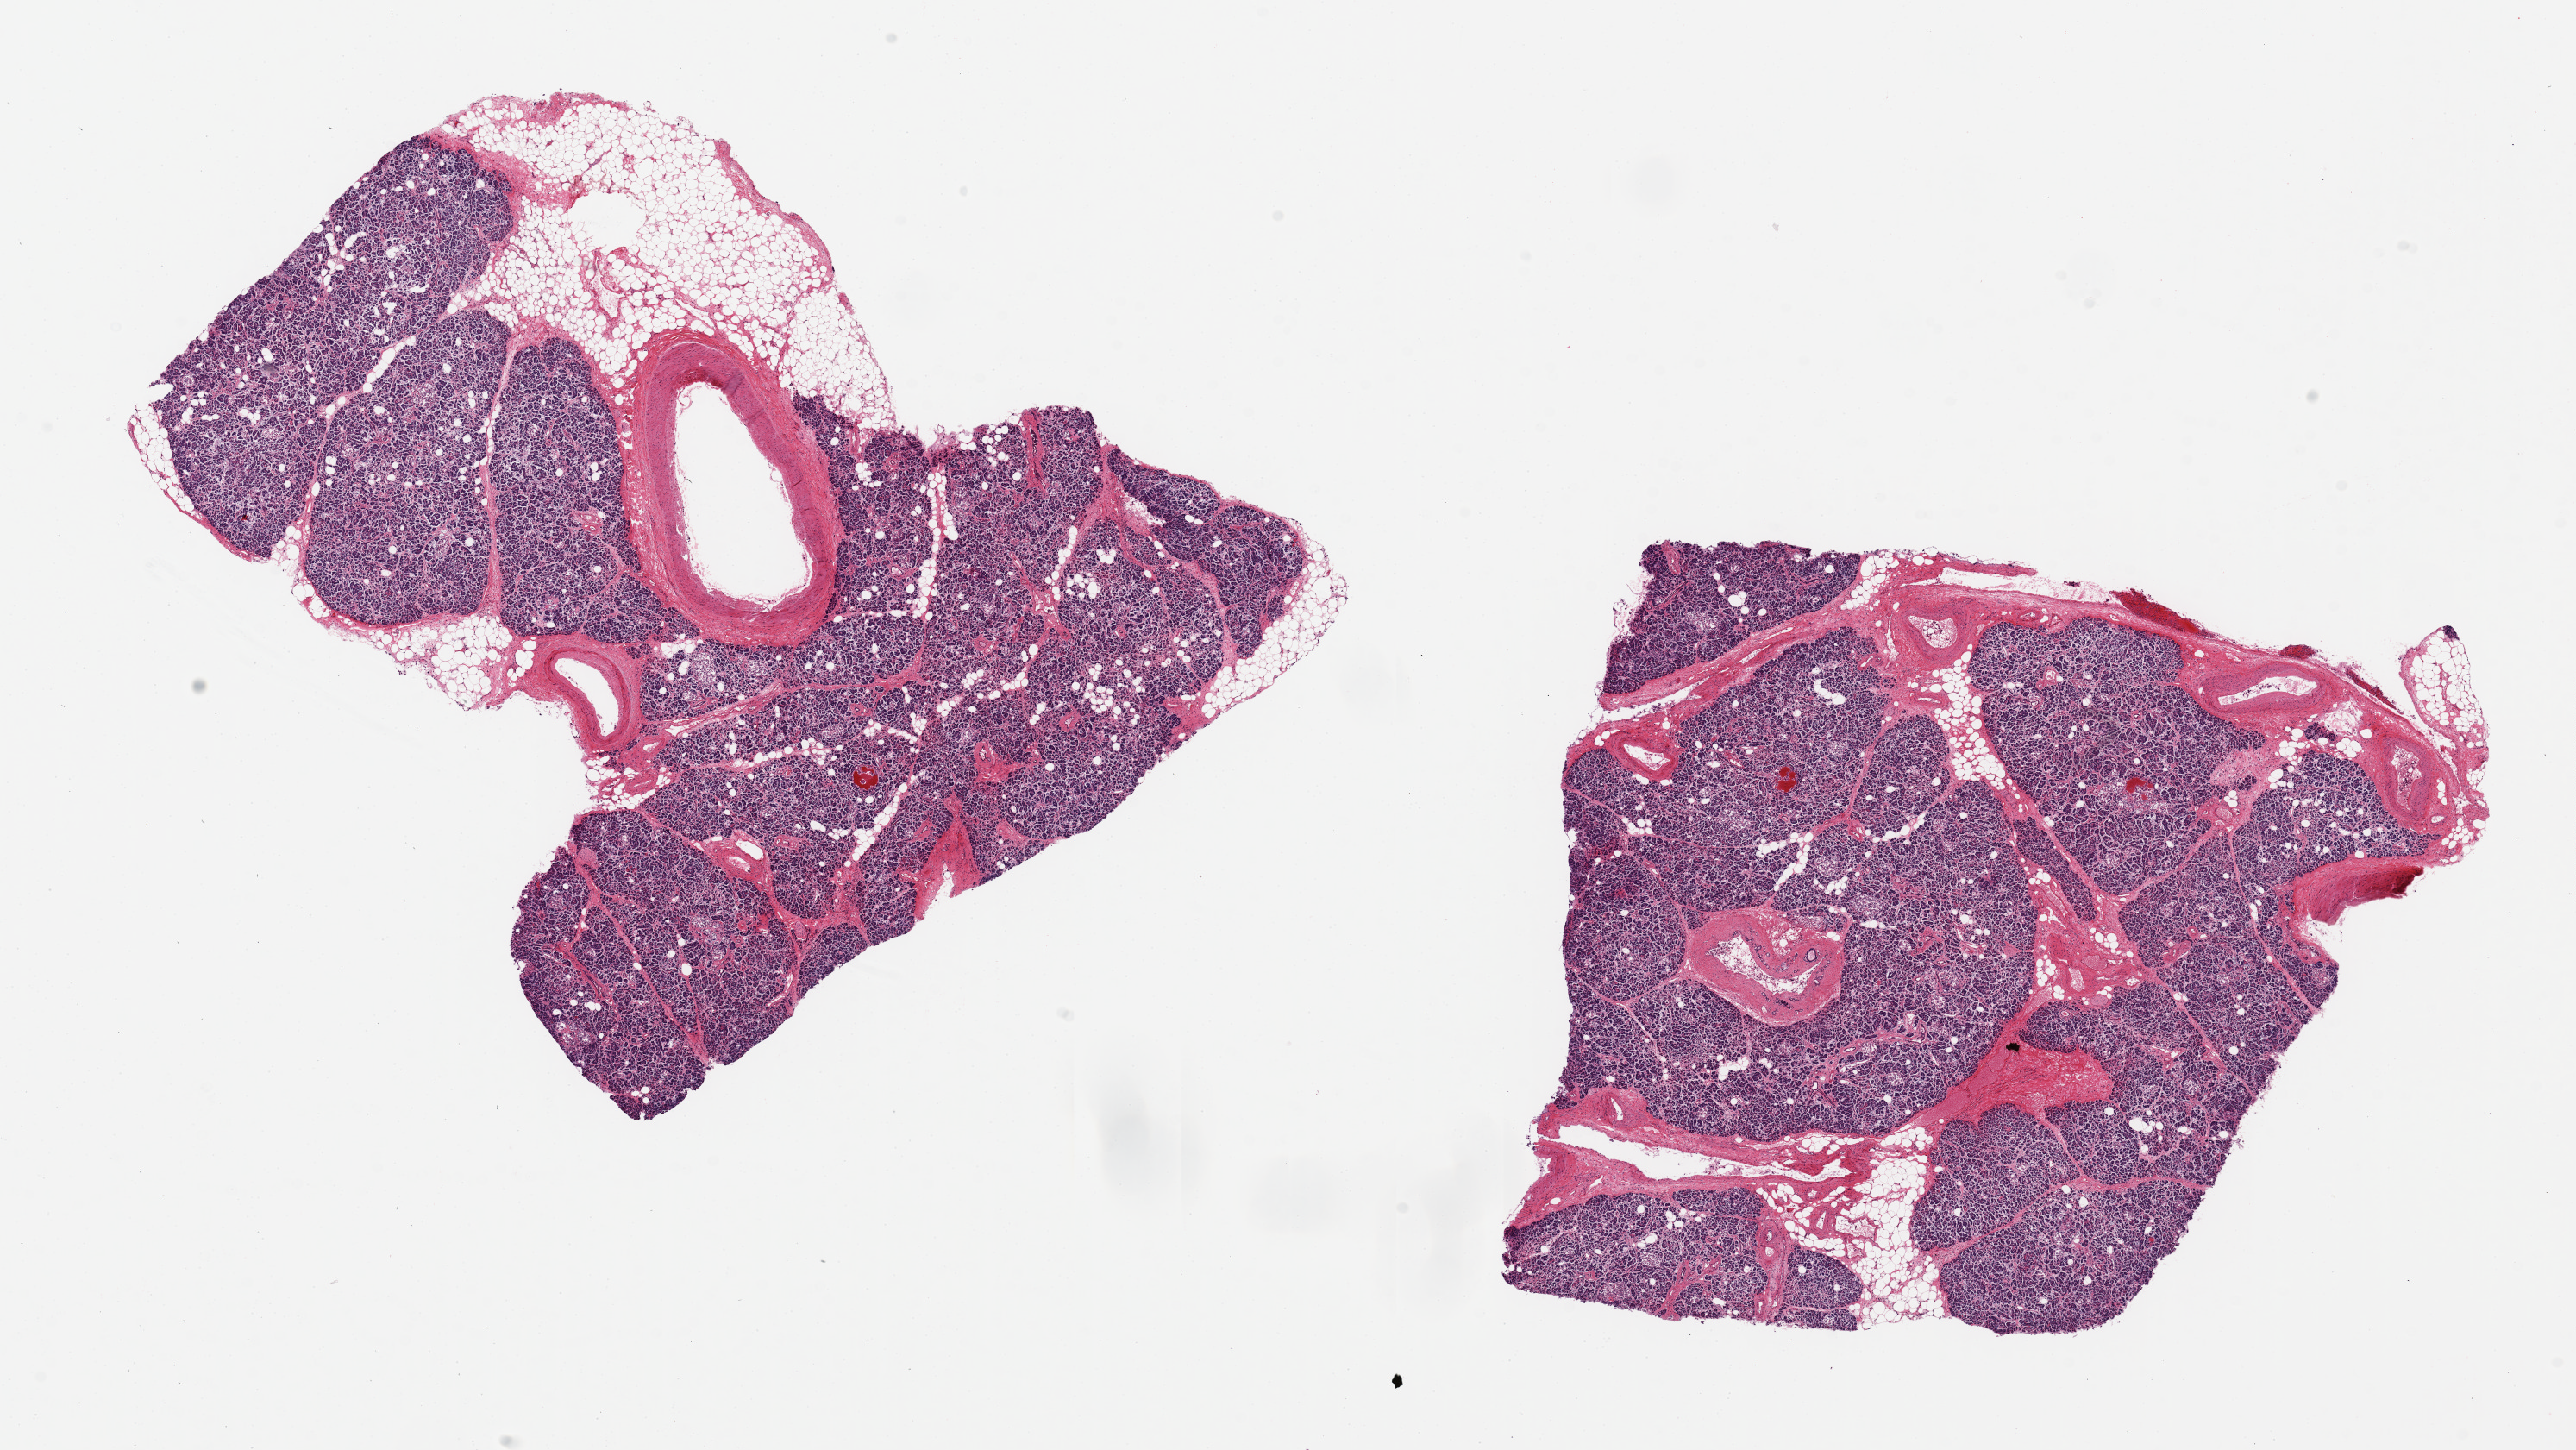
Haematoxylin and eosin whole-slide image, whole scanned area (about 23.6 x 13.3 mm, from a 20x scan) shown as a low-resolution overview; PAXgene-fixed paraffin-embedded (PFPE) section; target tissue: pancreas; tissue donor sample. Male donor.
Review note (as recorded): 2 pieces, 8x8 & 8x7mm; ~20% peripheral adipose in 1 piece; islets not sclerosed or reduced in number.